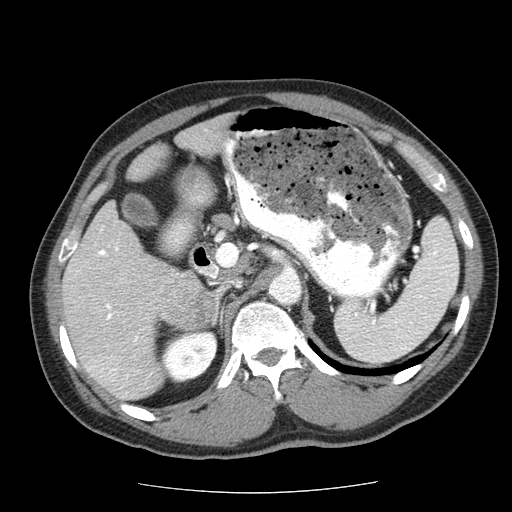
Contrast-enhanced abdominal CT (liver protocol), one axial slice. Position 29 of 85 along the scan axis. Soft-tissue window (W 400 / L 40 HU). 512 × 512 image matrix, field of view 360 × 360 mm. Case-level facts recorded for this patient, not image findings: diagnosis: hepatocellular carcinoma (patient treated with transarterial chemoembolisation; whether this scan precedes or follows treatment is not stated here); TNM stage (as recorded): Stage-IIIA; Child-Pugh class: A; tumour differentiation: well differentiated; tumour nodularity: multinodular.
Structures marked on this image (semi-automatically segmented with operator editing):
- liver parenchyma outside the tumour (the mass and vessels are separate outlines, so this box may not span the whole liver): bounding box <62,112,234,400> (left, top, right, bottom; pixels)
- mass: <157,274,213,333>
- liver vessels: <88,229,138,378>